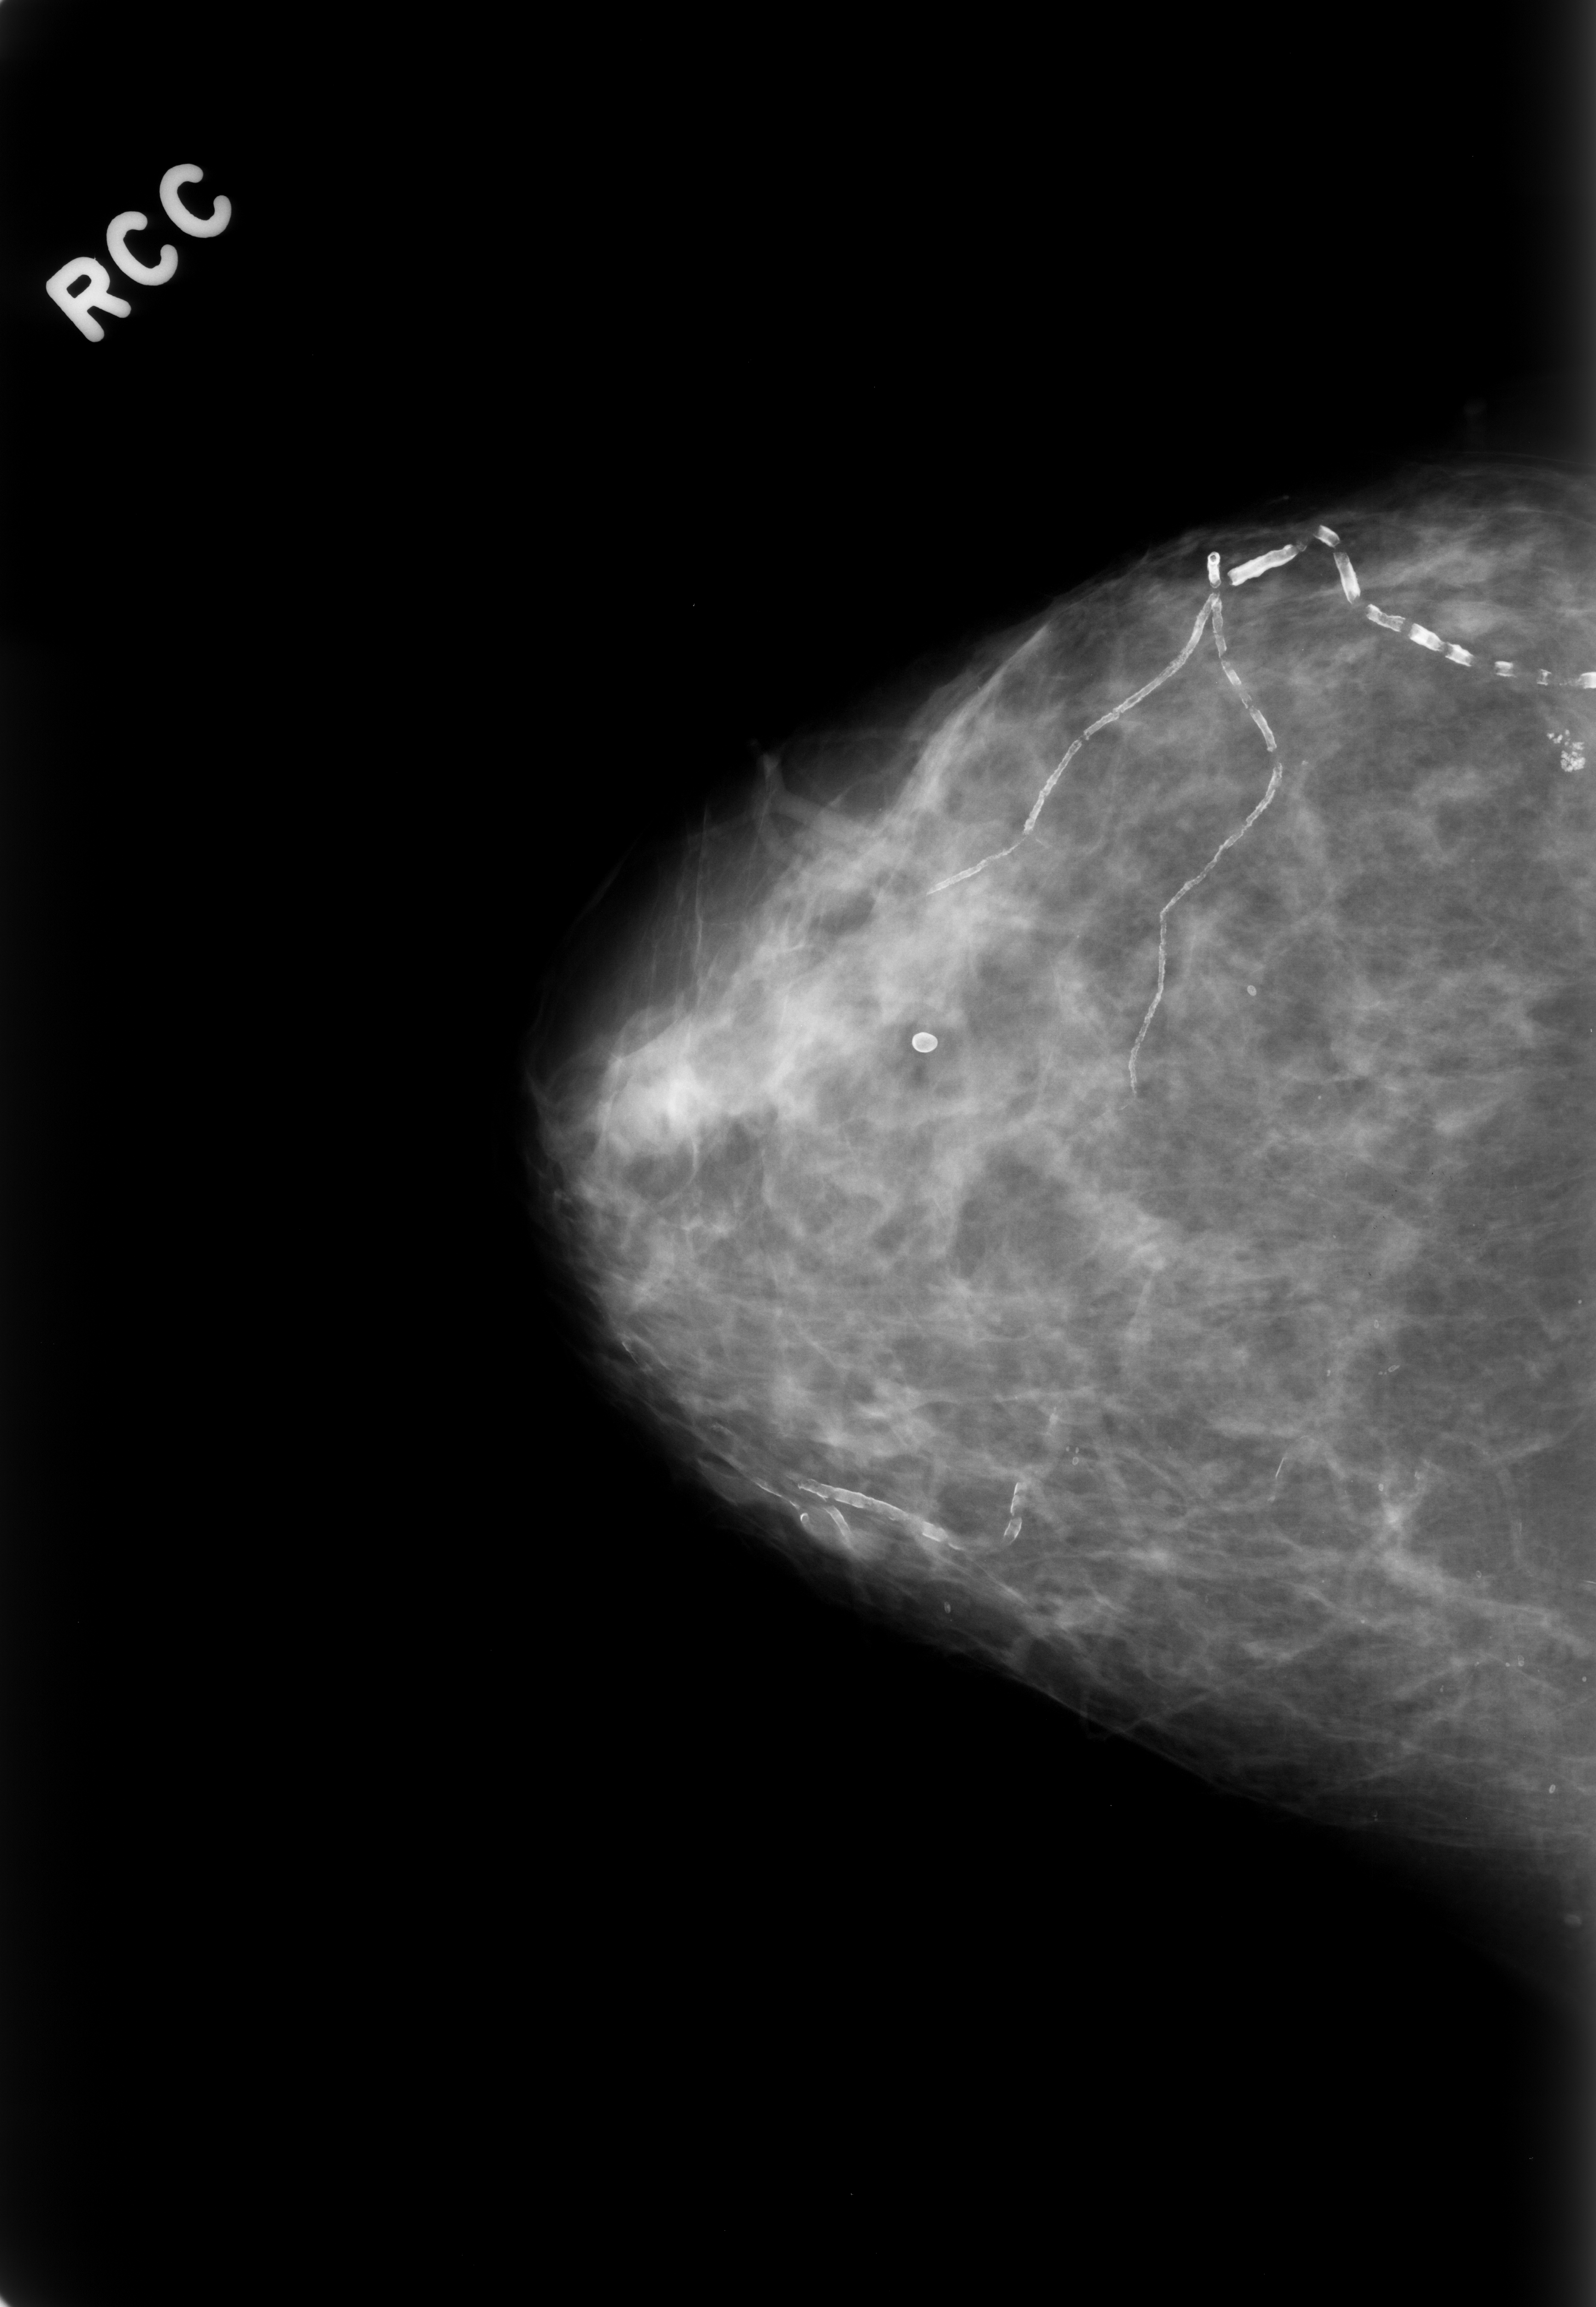
Scanned film-screen mammogram; right breast; craniocaudal (CC) view; BI-RADS breast density category 2 (scale 1–4); 1596 × 2307 image matrix.
Expert-marked regions of interest on this image (one box per marked abnormality):
- calcifications, morphology pleomorphic, distribution clustered; BI-RADS assessment category 4; subtlety rating 5 on a 1 (subtle) to 5 (obvious) scale; pathology result (as recorded, not read from the image): benign: bounding box (x1, y1, x2, y2) in pixels: (1514, 691, 1594, 797)